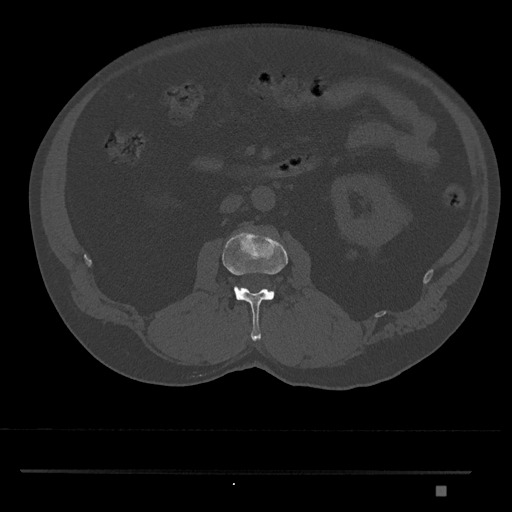
CT including the spine, one axial slice; slice 740 of 1134 in the series (ordered by position); bone window (W 1800 / L 400 HU); 0.5 mm slice thickness; 512 × 512 image matrix, field of view 429 × 429 mm. Male patient, age 65 years. From the clinical record (not read from this slice): primary cancer: prostate.
Annotated regions visible in this slice (semi-automatic segmentation, software-assisted and operator-edited):
- L2 vertebra: bounding box (x1, y1, x2, y2) in pixels: (222, 231, 288, 341)